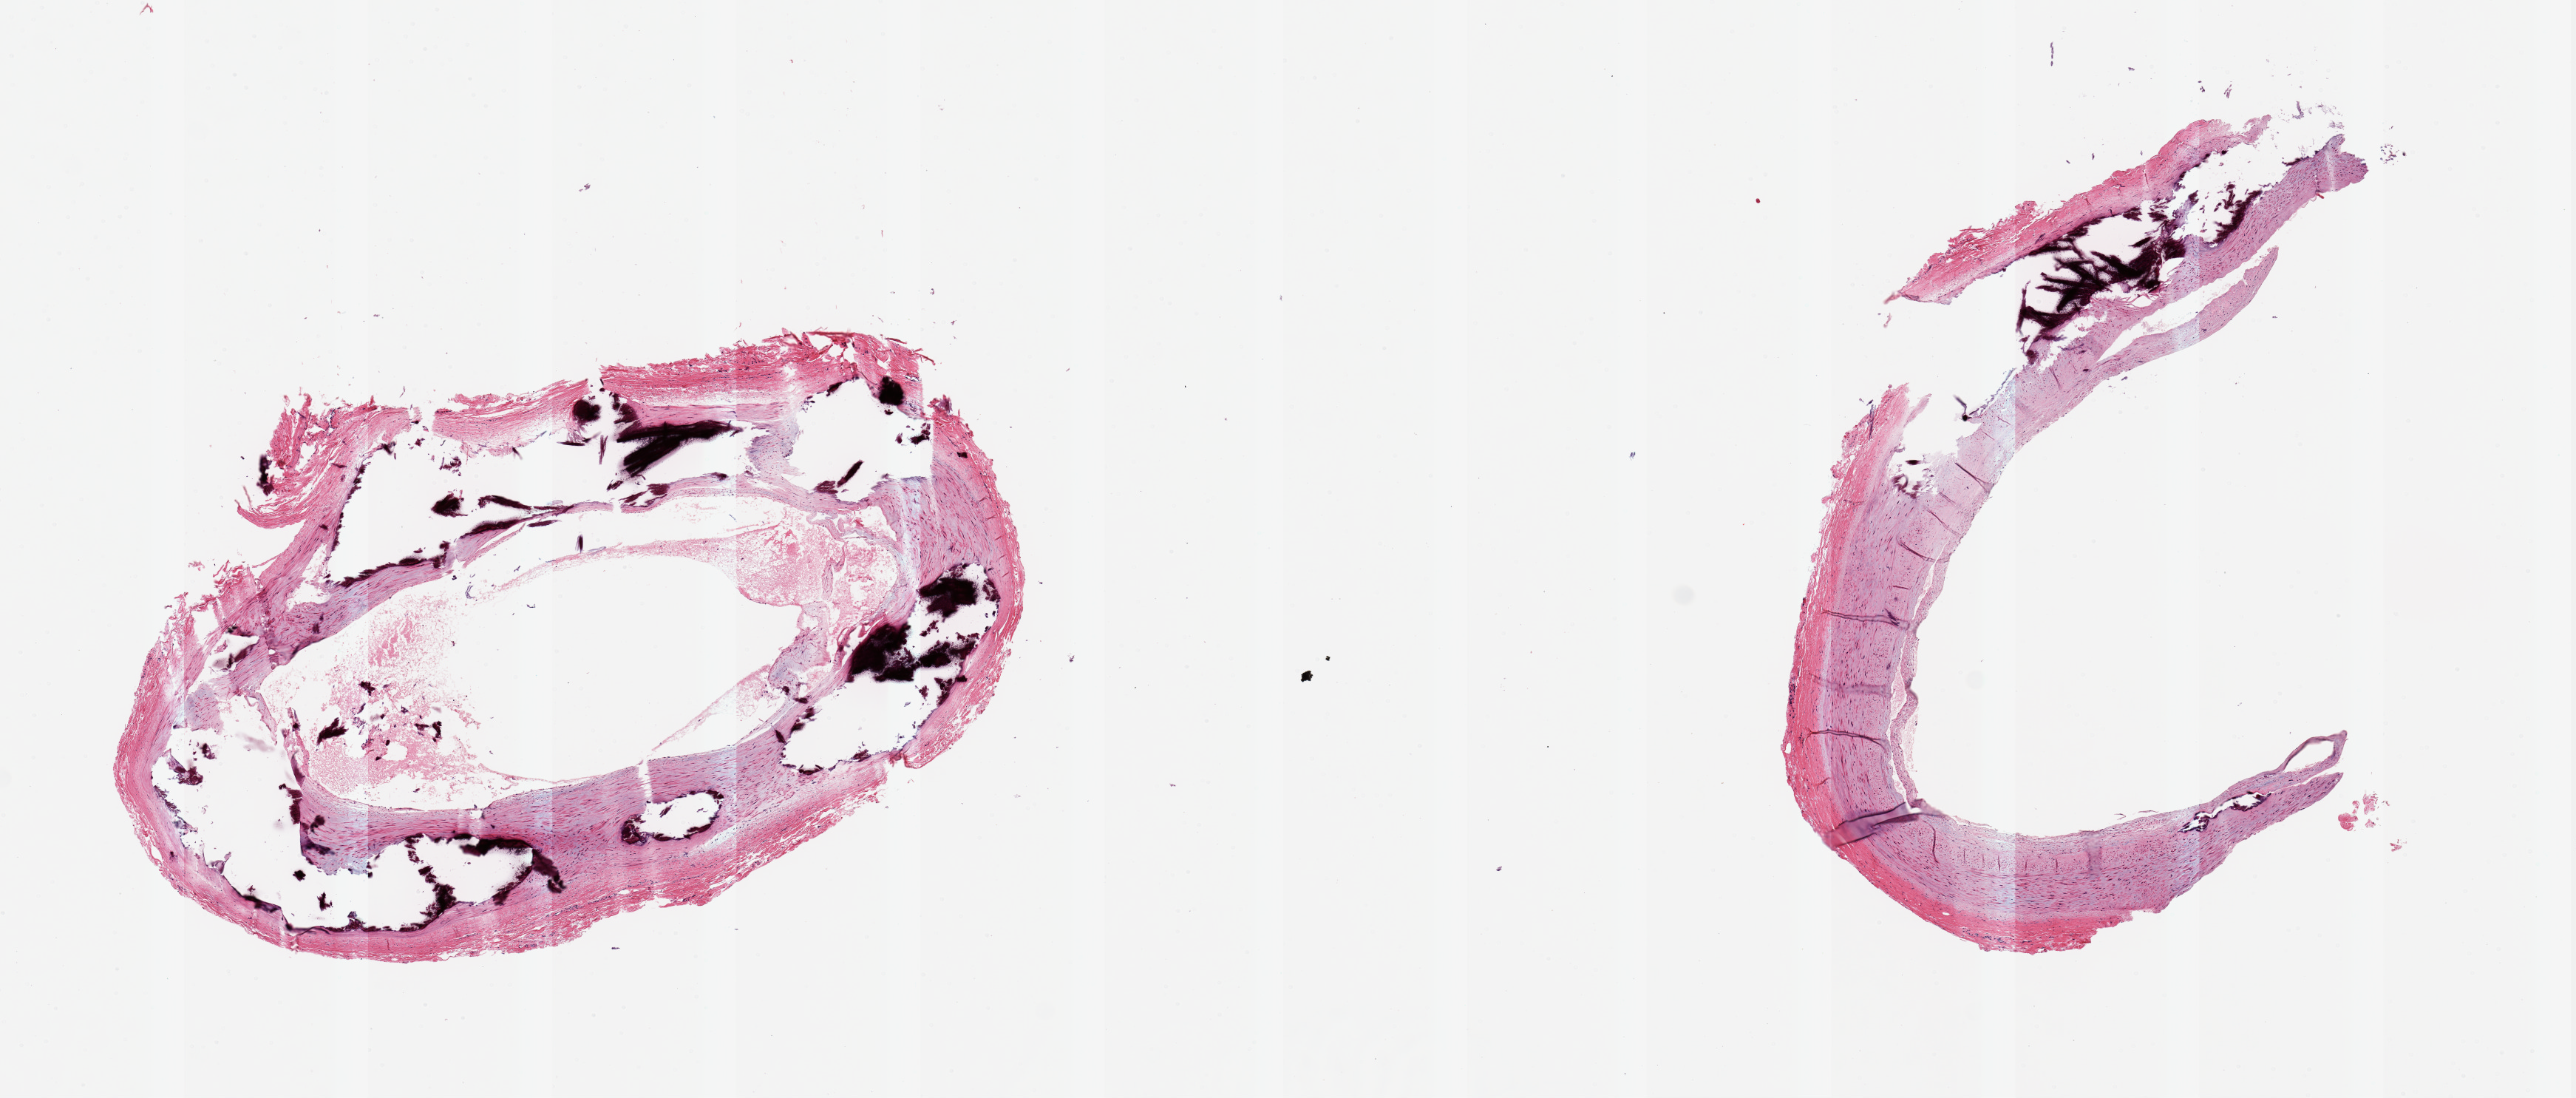
Haematoxylin and eosin whole-slide image — a low-resolution overview of the entire scanned area, about 13.8 x 5.9 mm (slide scanned at 20x); PAXgene-fixed, paraffin-embedded tissue; target tissue: tibial artery; tissue donor sample. Donor: female.
Reviewer comment on this tissue sample: 2 pieces, 5x1 & 5x3.5mm; heavily calcified; half of 1 piece without lesion.